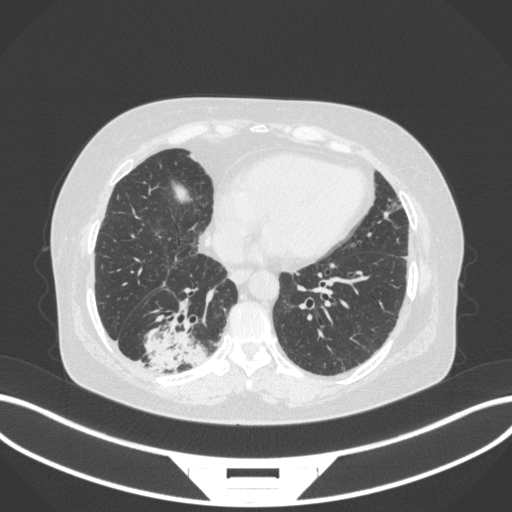
Chest CT, one axial slice. Slice 73 of 303 in the series (ordered by position). Reconstruction kernel B31f. 120 kVp. Lung window (W 1500 / L -600 HU). 512 × 512 image matrix. Female patient, age 65 years. From the clinical record (not read from this slice): clinical TNM (as recorded): T2b N1 M0; histopathological grade: G1.
Structures marked on this image (bounding box drawn by a radiologist):
- lung tumour (recorded histology: adenocarcinoma): bounding box (x1, y1, x2, y2) in pixels: (139, 324, 209, 373)